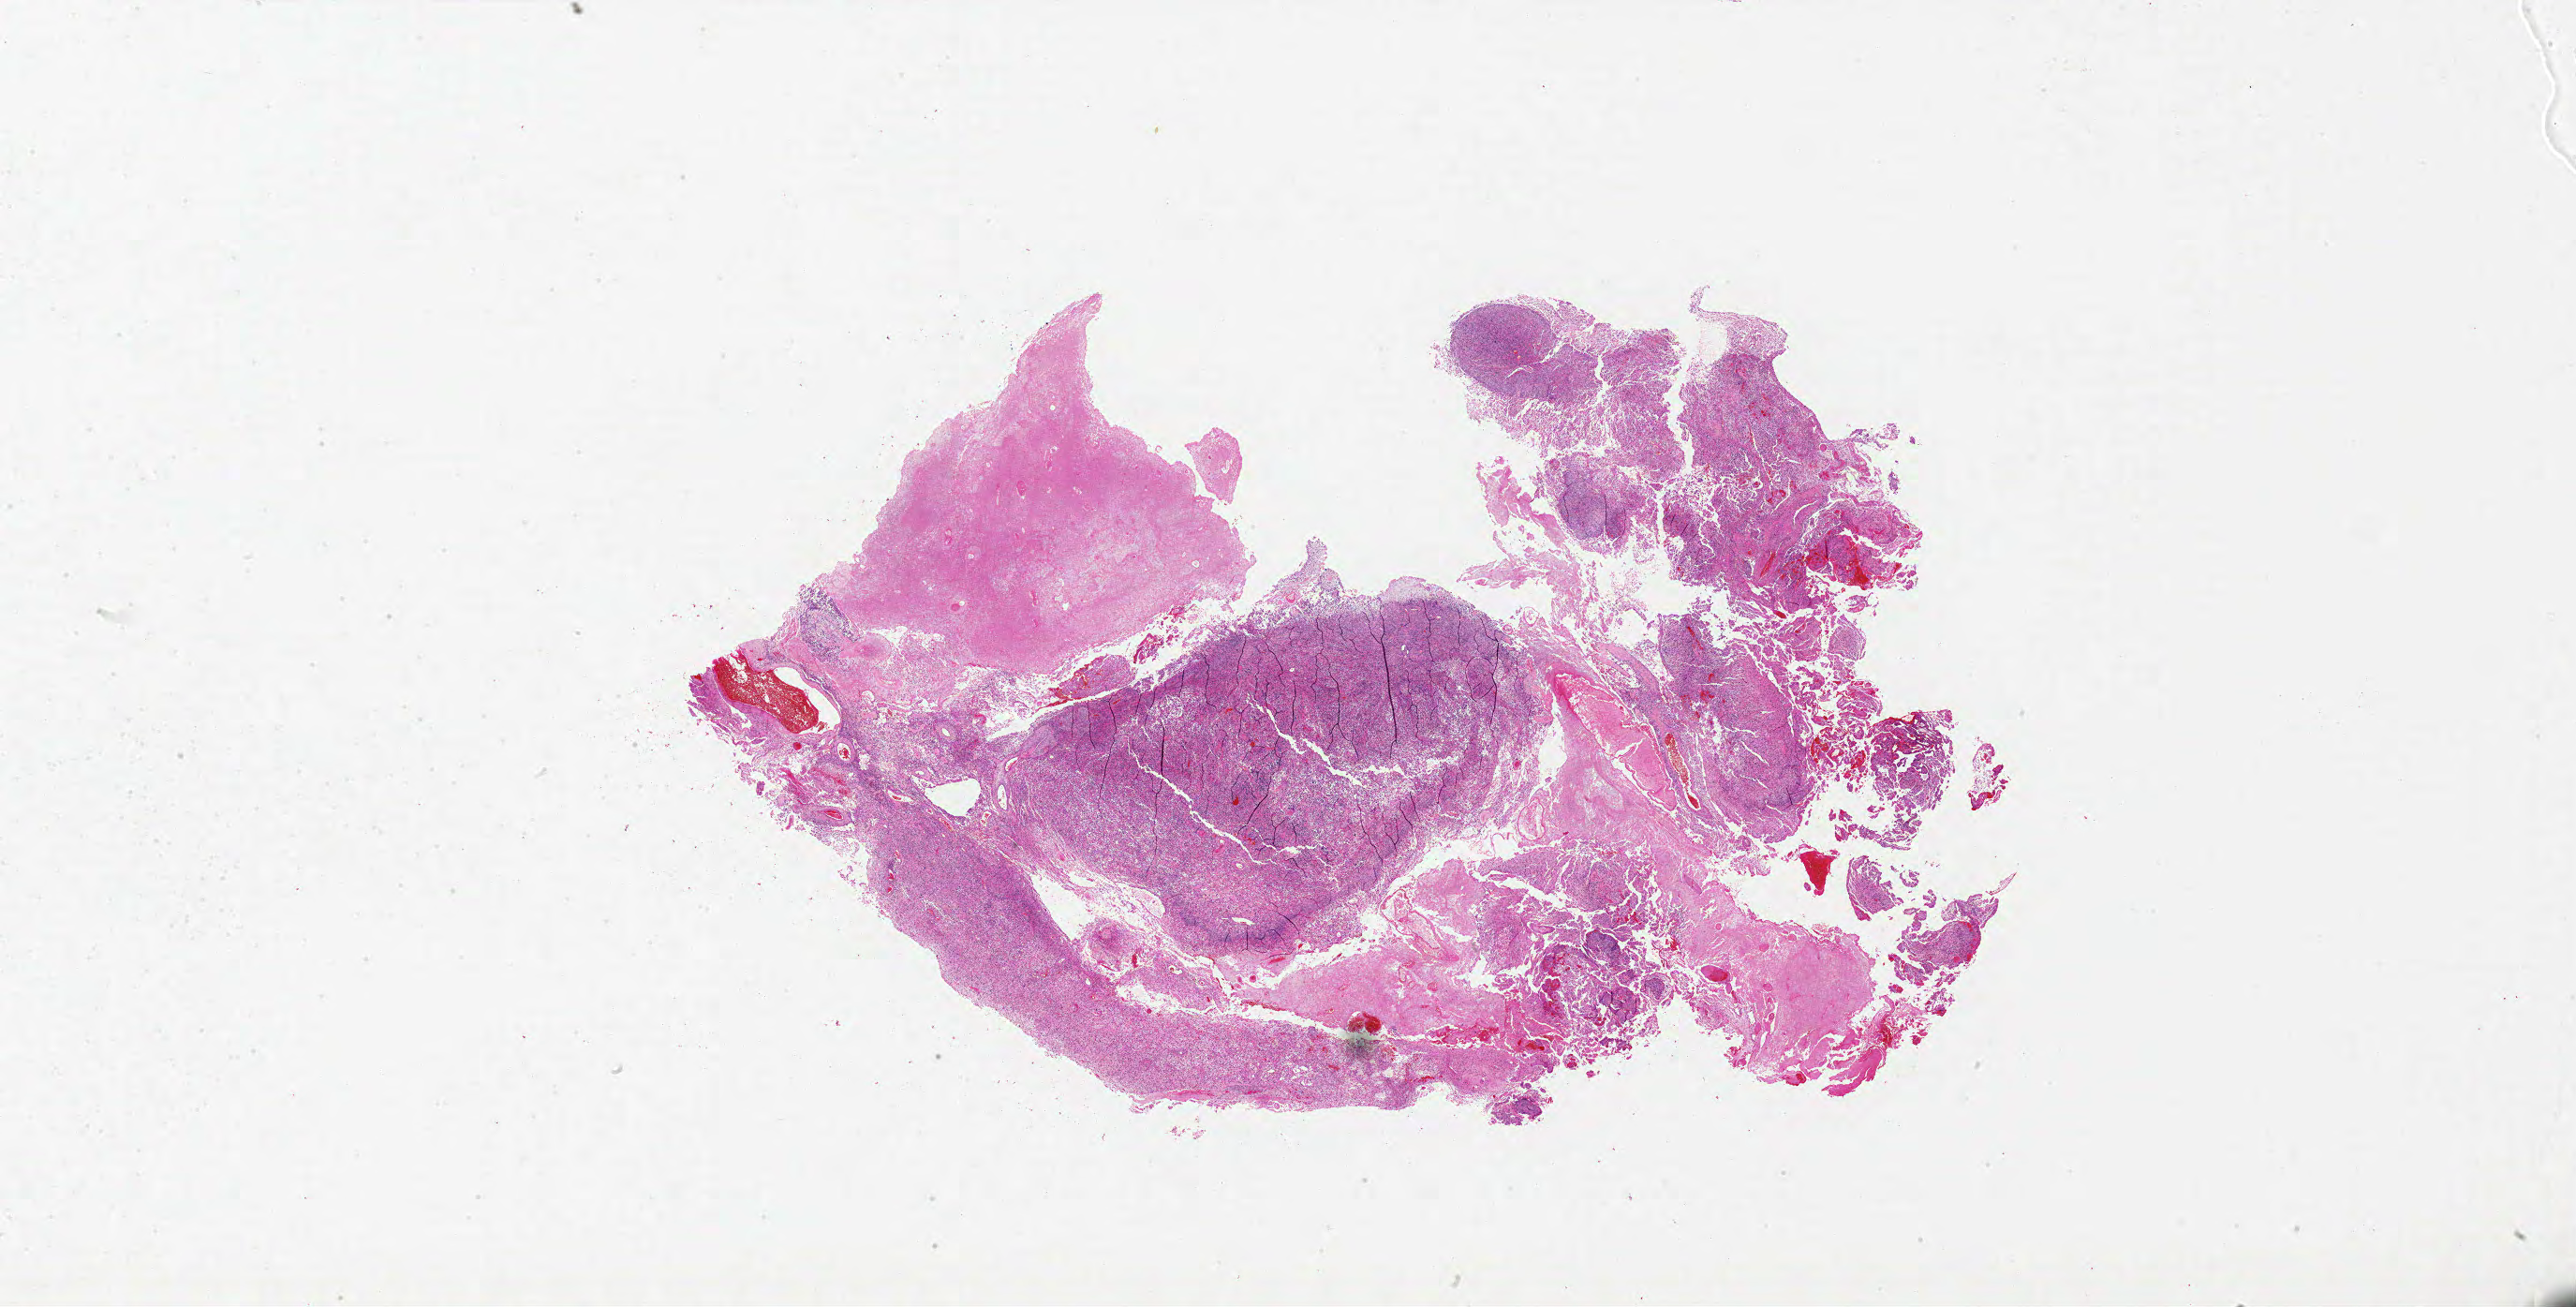
H&E whole-slide image, shown as a low-resolution overview of the whole scanned area (about 44.0 x 22.3 mm, slide scanned at 20x); FFPE section; brain, primary tumour sample. Female, age 68 years at initial diagnosis.
Histologic diagnosis: Glioblastoma.